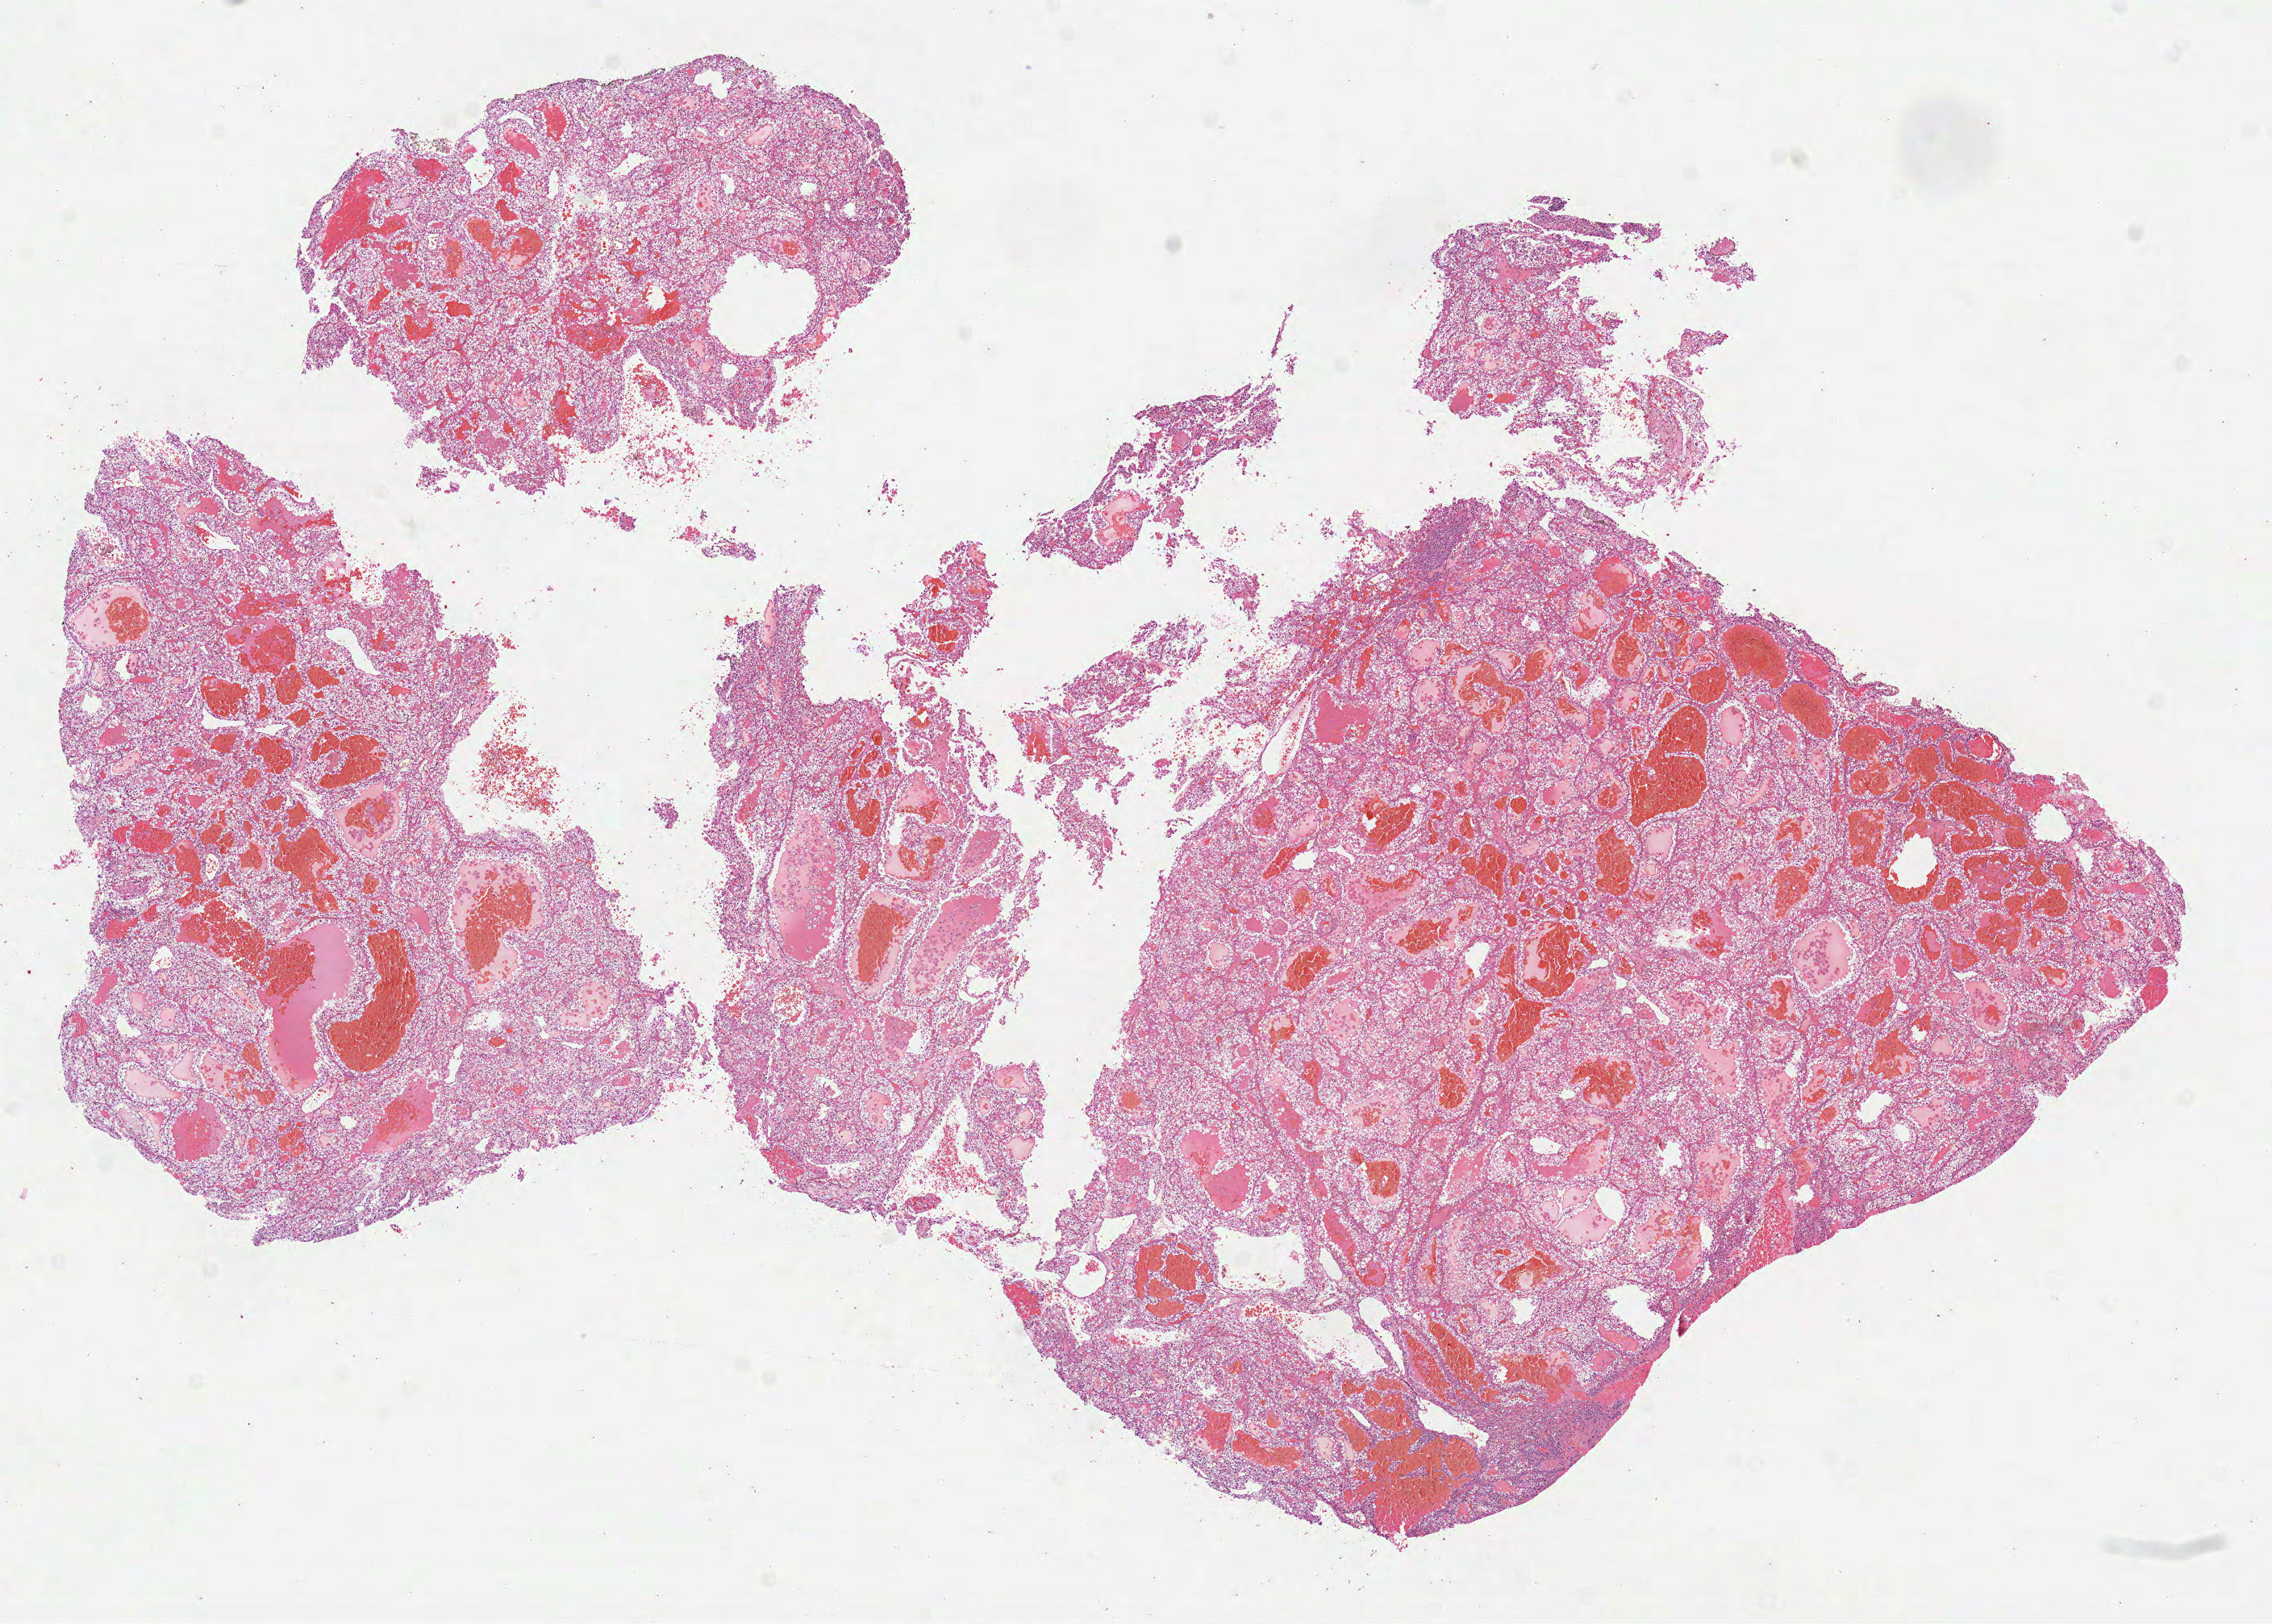
H&E whole-slide image, a low-resolution overview of the entire scanned area, about 11.4 x 8.1 mm, formalin-fixed paraffin-embedded (FFPE) diagnostic section, primary tumour sample from the kidney. Male patient; age at initial diagnosis 62 years. Histologic grade: G3 (poorly differentiated).
* diagnosis: Clear cell adenocarcinoma, NOS
* AJCC pathologic stage: II
* laterality: right